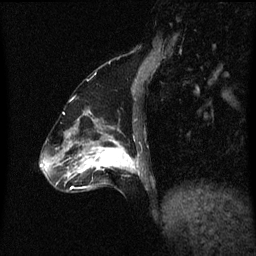
Breast MRI (dynamic contrast-enhanced), one sagittal slice. Slice 20 of 60 in the series (ordered by position). Dynamic contrast-enhanced series, image 2 of 3 at this slice position (ordered by acquisition). 1.5 T. TE 4.2 ms, TR 8.4 ms. 2 mm slice thickness. 256 × 256 image matrix. Female patient, age 47 years.
Outlined on this slice (semi-automatically segmented with operator editing):
- analysis volume of interest (the breast-tissue region the enhancement analysis was run in; not a lesion): box from (x=85, y=136) to (x=142, y=191) px
- tumour enhancement mask (voxels above the 70 % enhancement threshold inside the analysis volume of interest): (x=85, y=140)–(x=139, y=171)